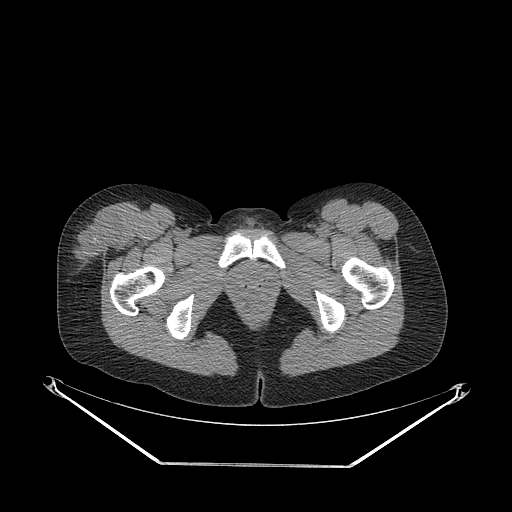
CT of an extremity soft-tissue mass (from a PET/CT study), one axial slice. Position 58 of 267 along the scan axis. 140 kVp. Soft-tissue window (W 400 / L 40 HU). 3.75 mm slice thickness. 512 × 512 image matrix. Female patient. Case-level facts recorded for this patient, not image findings: histological type: synovial sarcoma; grade: intermediate; site of the primary tumour: right thigh.
Outlined on this slice (expert contour drawn on MRI and transferred to this co-registered scan by the dataset authors):
- gross tumour volume including surrounding oedema: bounding box [x1, y1, x2, y2] px = [71, 212, 122, 261]
- gross tumour volume (mass): [71, 212, 122, 261]